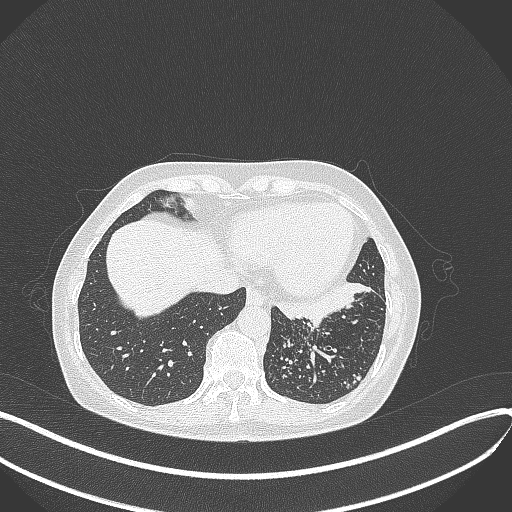
Chest CT, one axial slice; position 106 of 429 along the scan axis; reconstruction kernel B70f; 100 kVp; lung window (W 1500 / L -600 HU); 512 × 512 image matrix. Female patient, age 63 years. From the clinical record (not read from this slice): clinical TNM (as recorded): T1b N0 M0.
Structures marked on this image (bounding box drawn by a radiologist):
- lung tumour (recorded histology: adenocarcinoma): bounding box <272,278,373,326> (left, top, right, bottom; pixels)